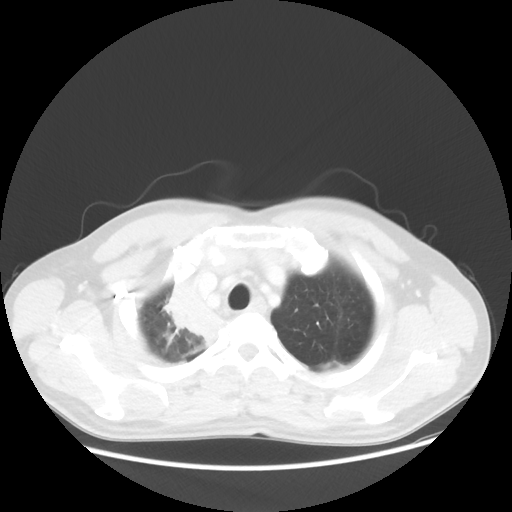
Chest CT, one axial slice; slice 47 of 56 in the series (ordered by position); reconstruction kernel STANDARD; lung window (W 1500 / L -600 HU); 5 mm slice thickness; 512 × 512 image matrix, field of view 398 × 398 mm. Patient: male, 60 years. From the clinical record (not read from this slice): clinical TNM (as recorded): T2a N1 M0.
Annotated regions visible in this slice (bounding box drawn by a radiologist):
- lung tumour (recorded histology: squamous cell carcinoma): box from (x=155, y=263) to (x=237, y=371) px